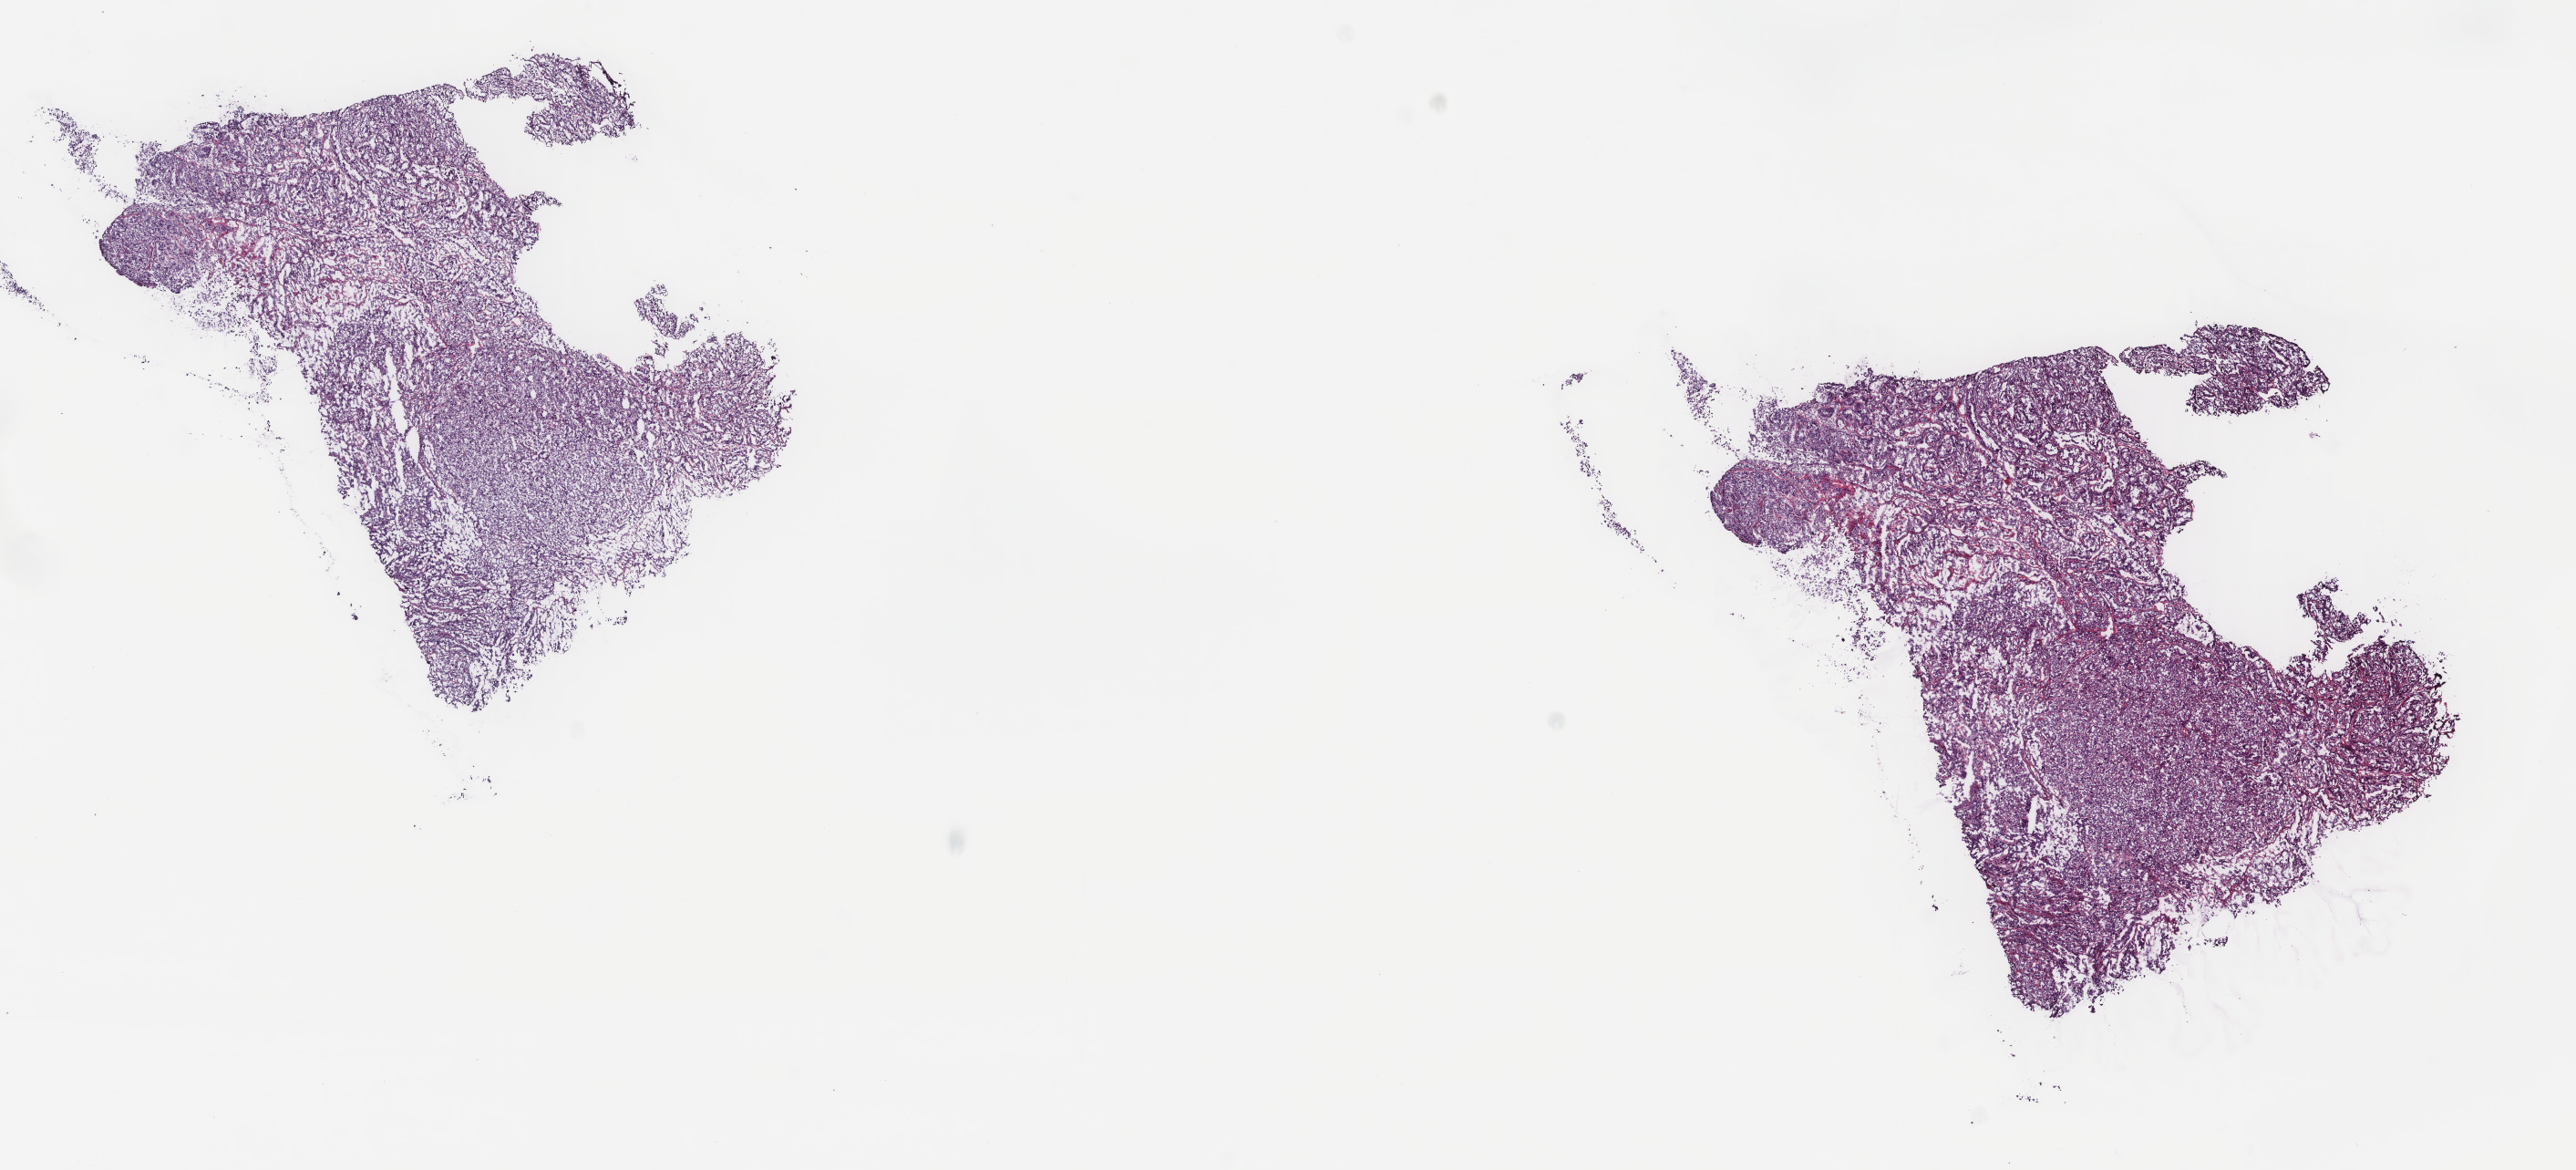
H&E whole-slide image, a low-resolution overview of the entire scanned area, about 22.4 x 10.2 mm (from a 40x scan); frozen section from the top of the tissue portion; sample: primary tumour, uterus. Patient: female, age at initial diagnosis 76 years. Histologic grade: G3 (poorly differentiated). Slide review estimates, as recorded: tumour cells 90%, tumour nuclei 90%, normal cells 0%, stromal cells 5%, necrosis 5%. Inflammatory infiltration, as recorded: lymphocyte infiltration 60%, monocyte infiltration 20%, neutrophil infiltration 10%.
FIGO stage: IA. Pathologic diagnosis: Serous cystadenocarcinoma, NOS (endometrium).